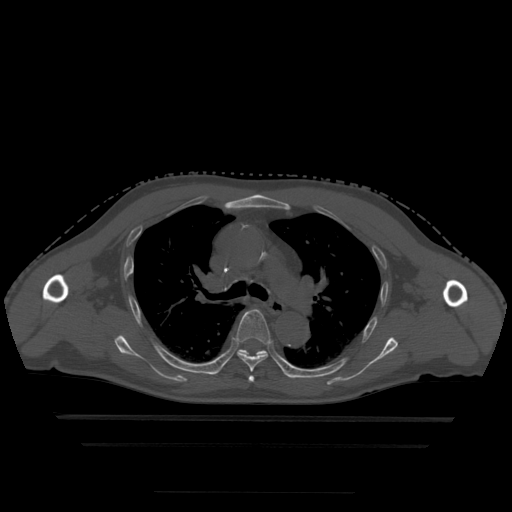
CT including the spine, one axial slice. Slice 333 of 522 in the series (ordered by position). Bone window (W 1800 / L 400 HU). 1.25 mm slice thickness. 512 × 512 image matrix, field of view 436 × 436 mm. Patient age 68 years. Case-level facts recorded for this patient, not image findings: primary cancer: urothelial.
Outlined on this slice (semi-automatic segmentation, software-assisted and operator-edited):
- T4 vertebra: bounding box [x1, y1, x2, y2] px = [248, 376, 255, 383]
- T5 vertebra: [236, 310, 272, 373]
- T6 vertebra: [239, 350, 267, 356]